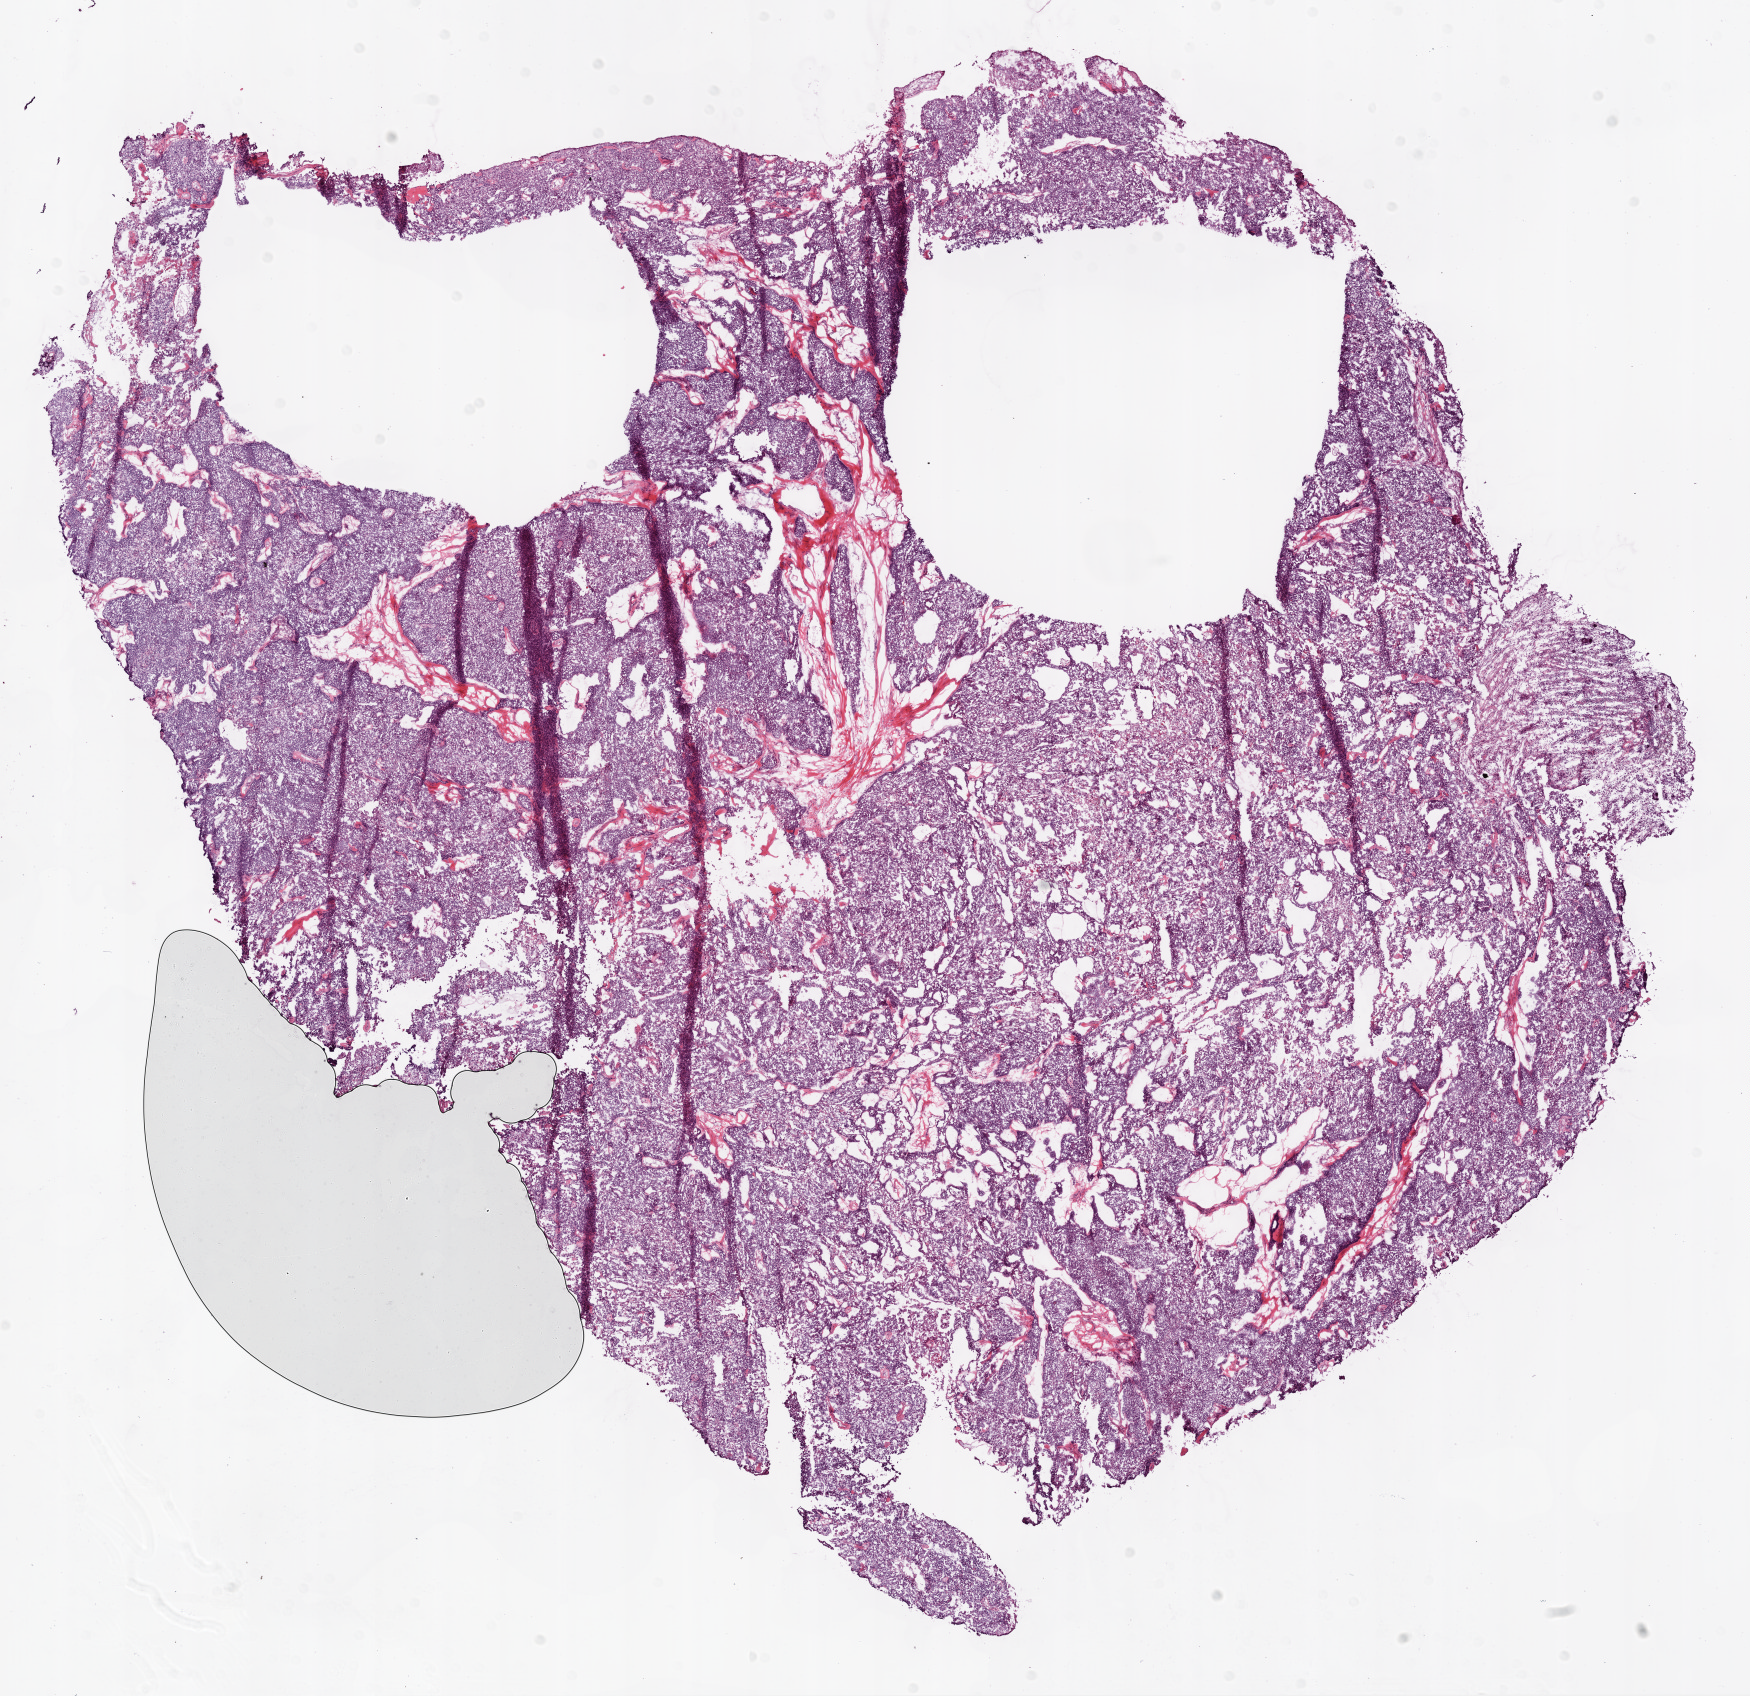
H&E-stained whole-slide image, whole scanned area (about 14.0 x 13.6 mm, acquisition: 20x scan) shown as a low-resolution overview; frozen section; sample: primary tumour, ovary. Female, age 84 years at initial diagnosis. Histologic grade: G3 (poorly differentiated). Pathologist review of this section (percent, as recorded): tumour cells 98%, tumour nuclei 95%, normal cells 0%, stromal cells 0%, necrosis 2%.
* laterality: right
* FIGO stage: IIIC
* diagnosis: Serous cystadenocarcinoma, NOS